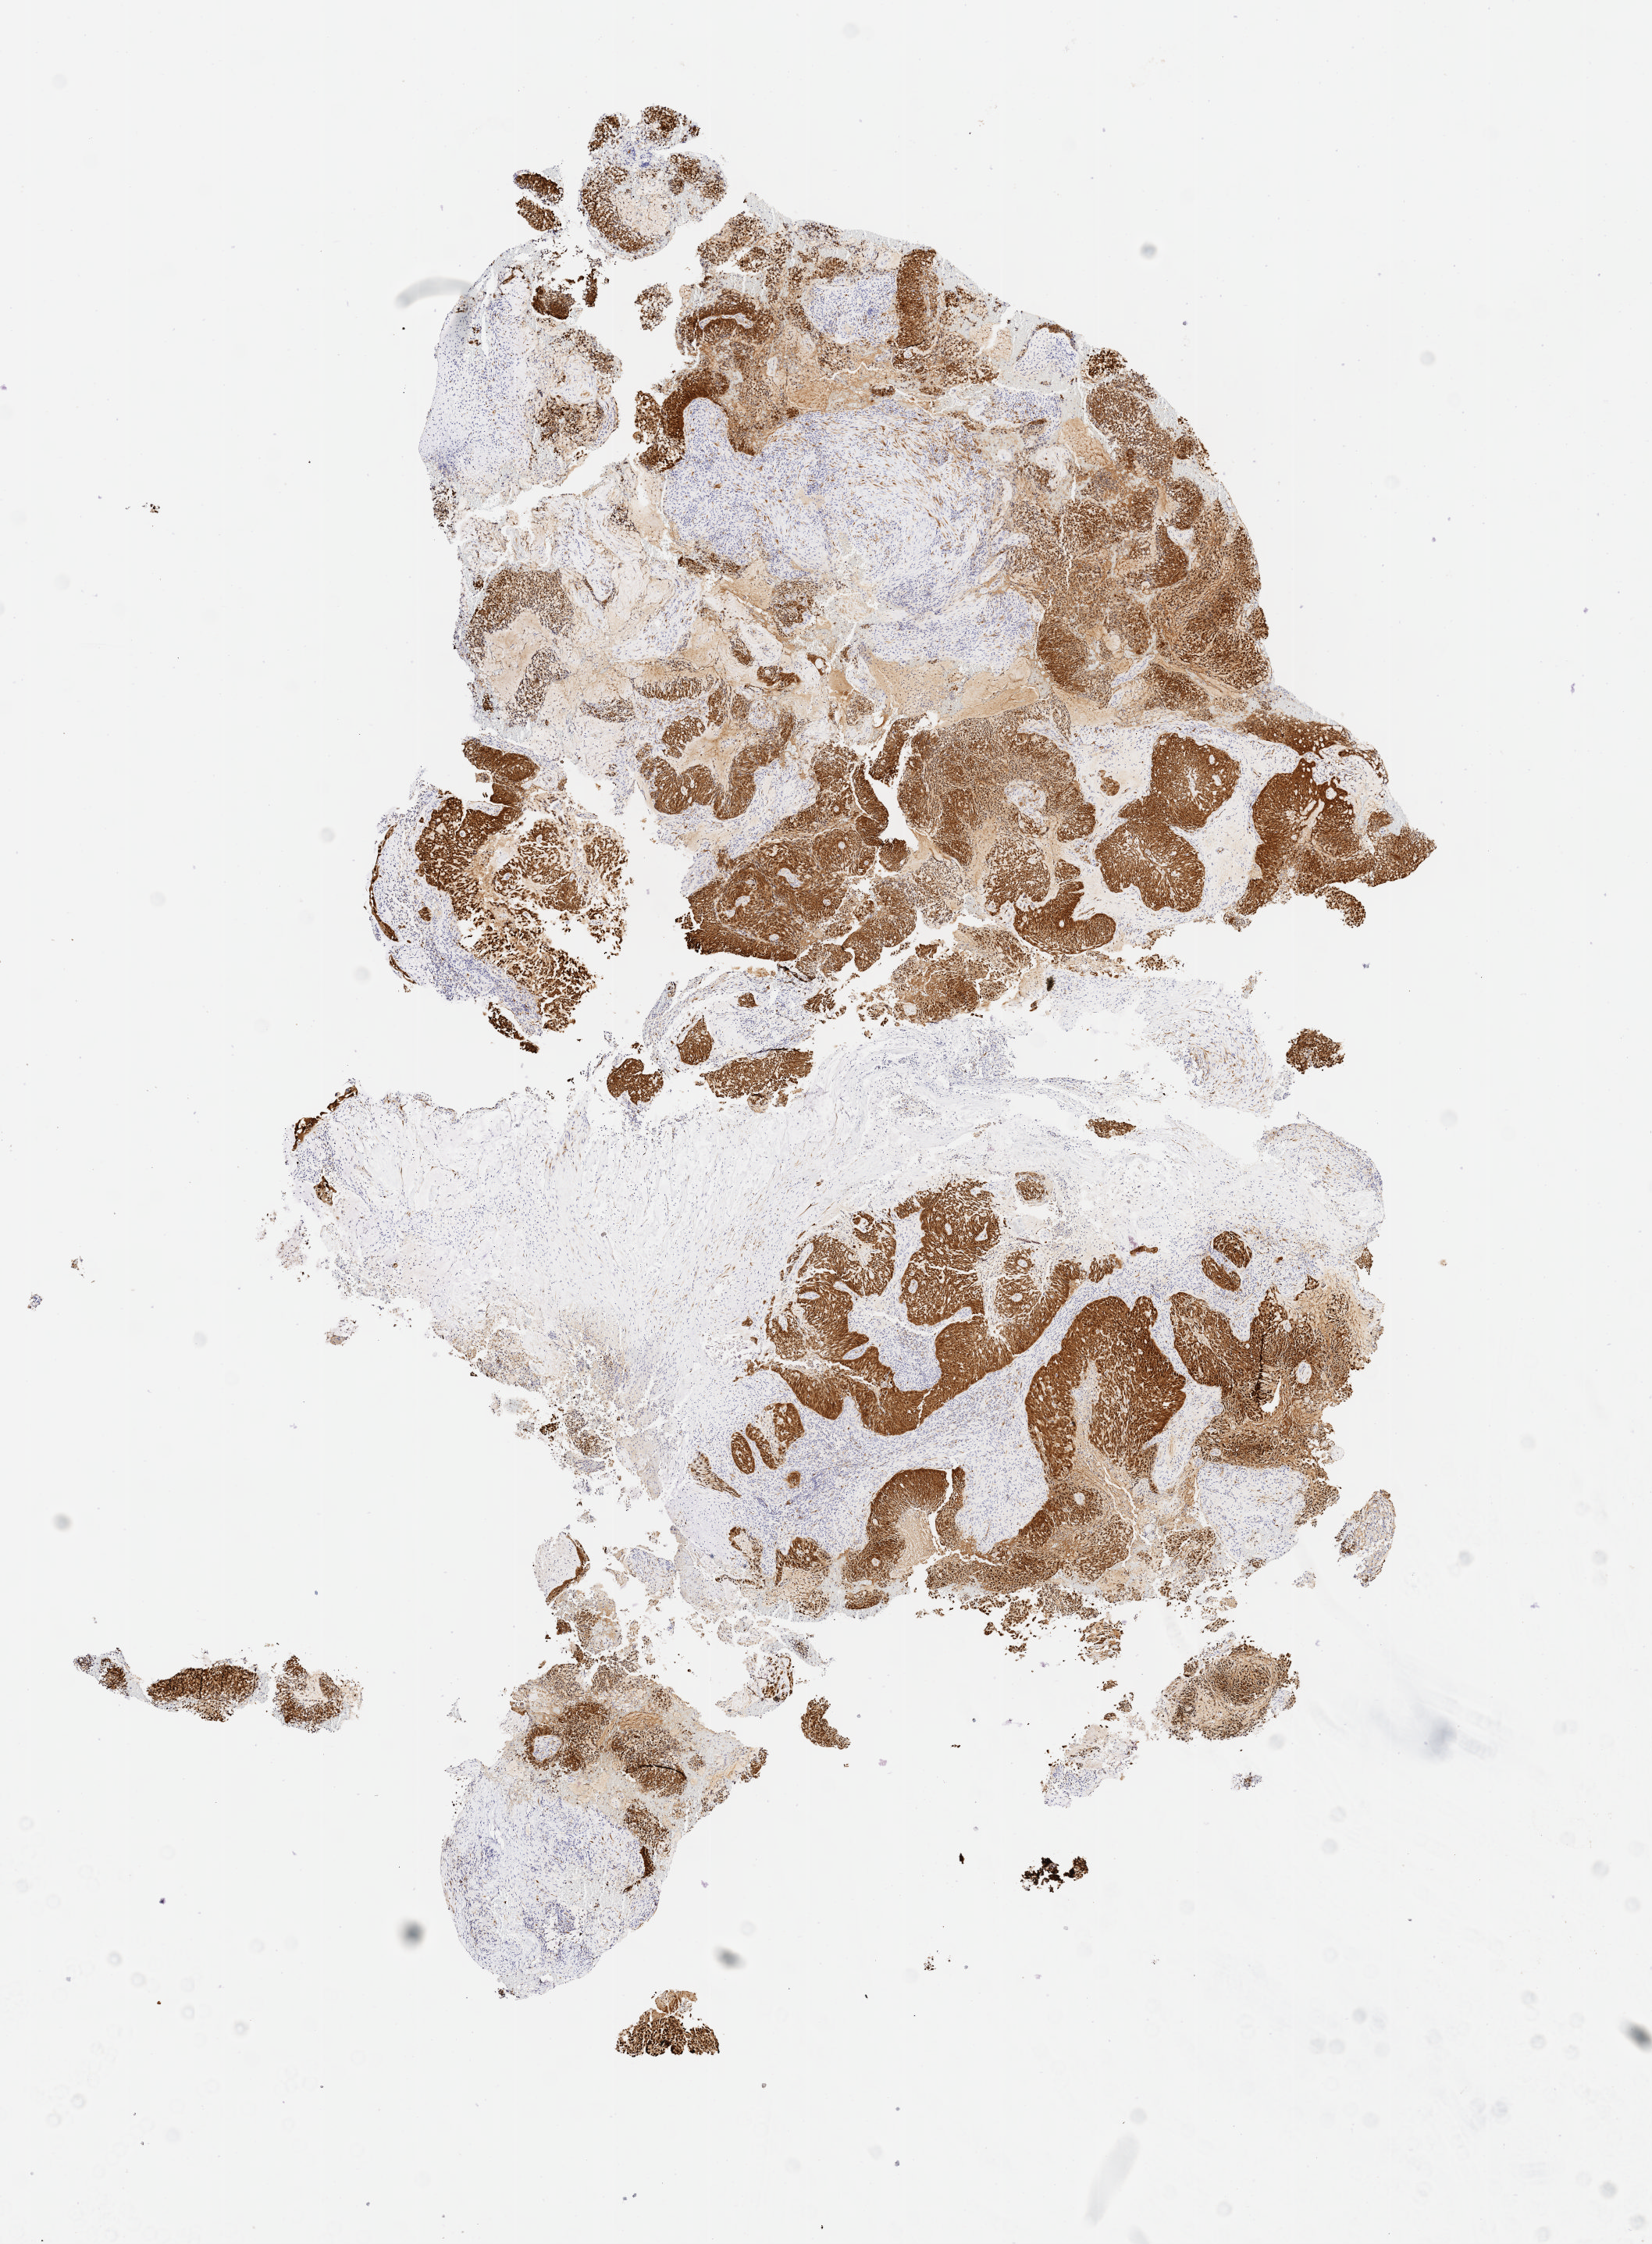
Whole-slide image, immunohistochemical stain for p16 (p16INK4a) — whole scanned area (about 8.6 x 11.6 mm) shown as a low-resolution overview; specimen: tumor tissue; anatomic site: cervix. Female patient, 69 years old.
* histologic diagnosis: Squamous cell carcinoma, large cell, nonkeratinizing, NOS